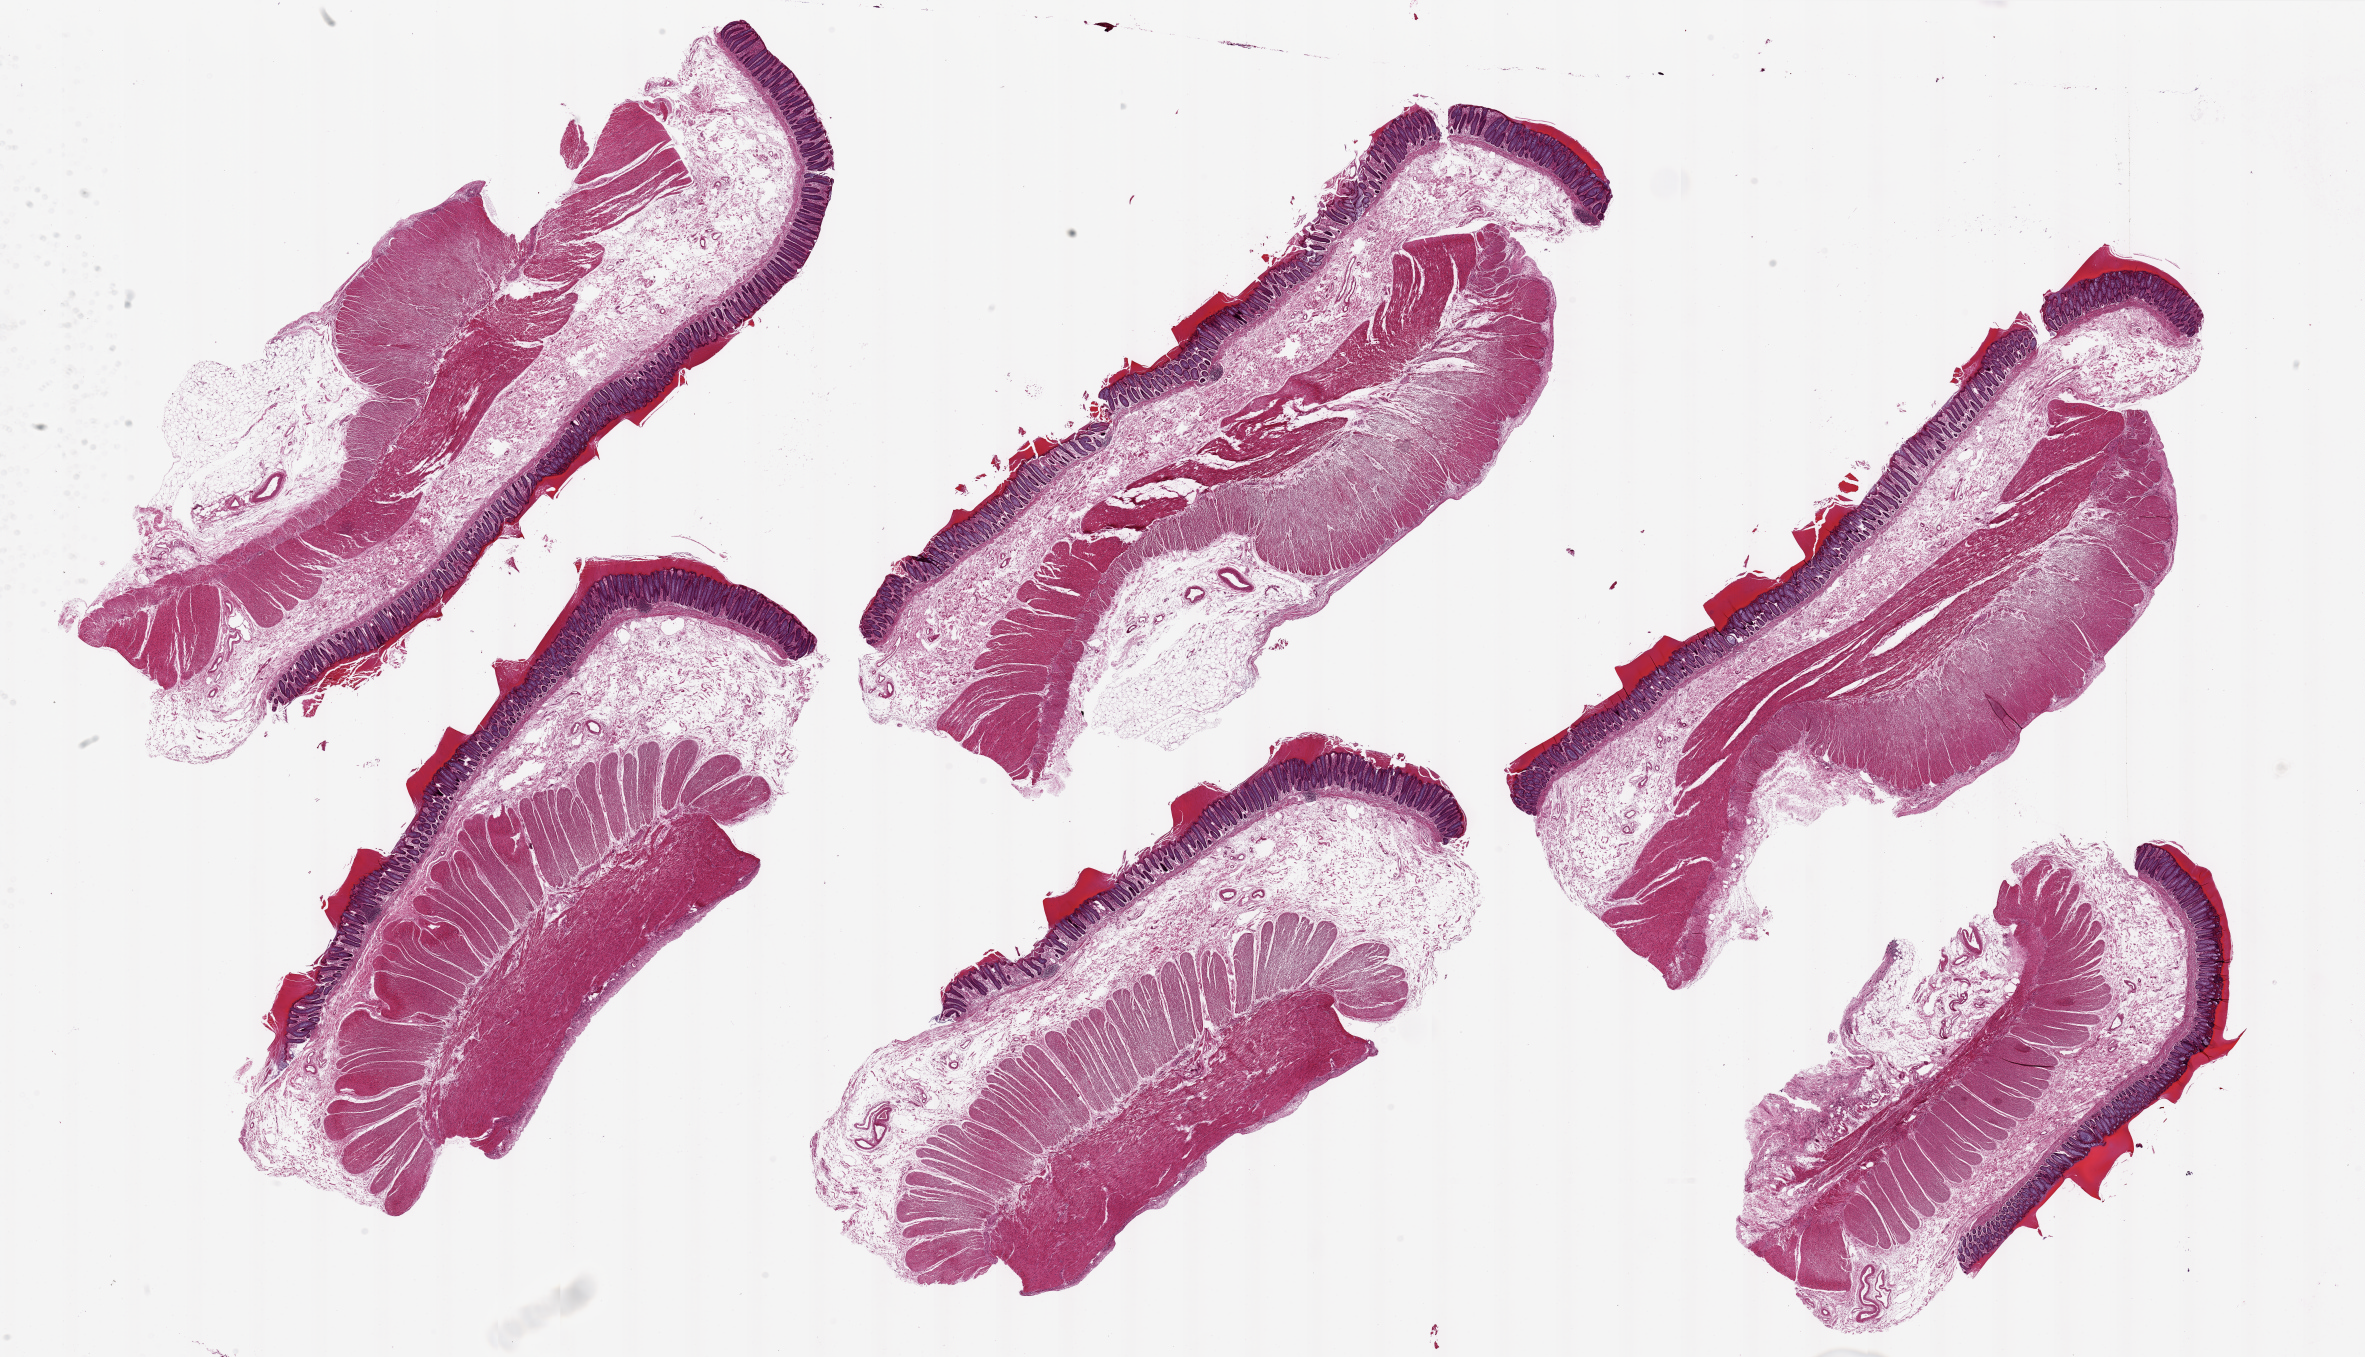
Whole-slide image, H&E stain, brightfield — low-resolution overview of the scanned area, about 37.4 x 21.5 mm (acquisition: 20x scan); PAXgene-fixed, paraffin-embedded tissue; sampled site (target tissue): sigmoid colon; donor tissue sample. Female donor.
Review note (as recorded): 6 pieces, up to 15x6mm; all 6 have full thickness of colon (target is muscle only).